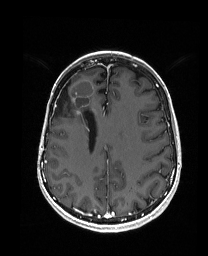
Brain MRI from a brain-tumour surgery series, one axial slice. Slice 67 of 192 in the series (ordered by position). T1-weighted post-contrast. 1 mm slice thickness. 208 × 256 image matrix, field of view 203 × 250 mm. Case-level facts recorded for this patient, not image findings: histopathology: Metastatic Carcinoma from Breast primary; tumour location: Right Frontal.
Outlined on this slice (outlined manually by an expert reader):
- previous resection cavity: box from (x=54, y=82) to (x=71, y=115) px
- tumour: (x=78, y=79)–(x=101, y=116)